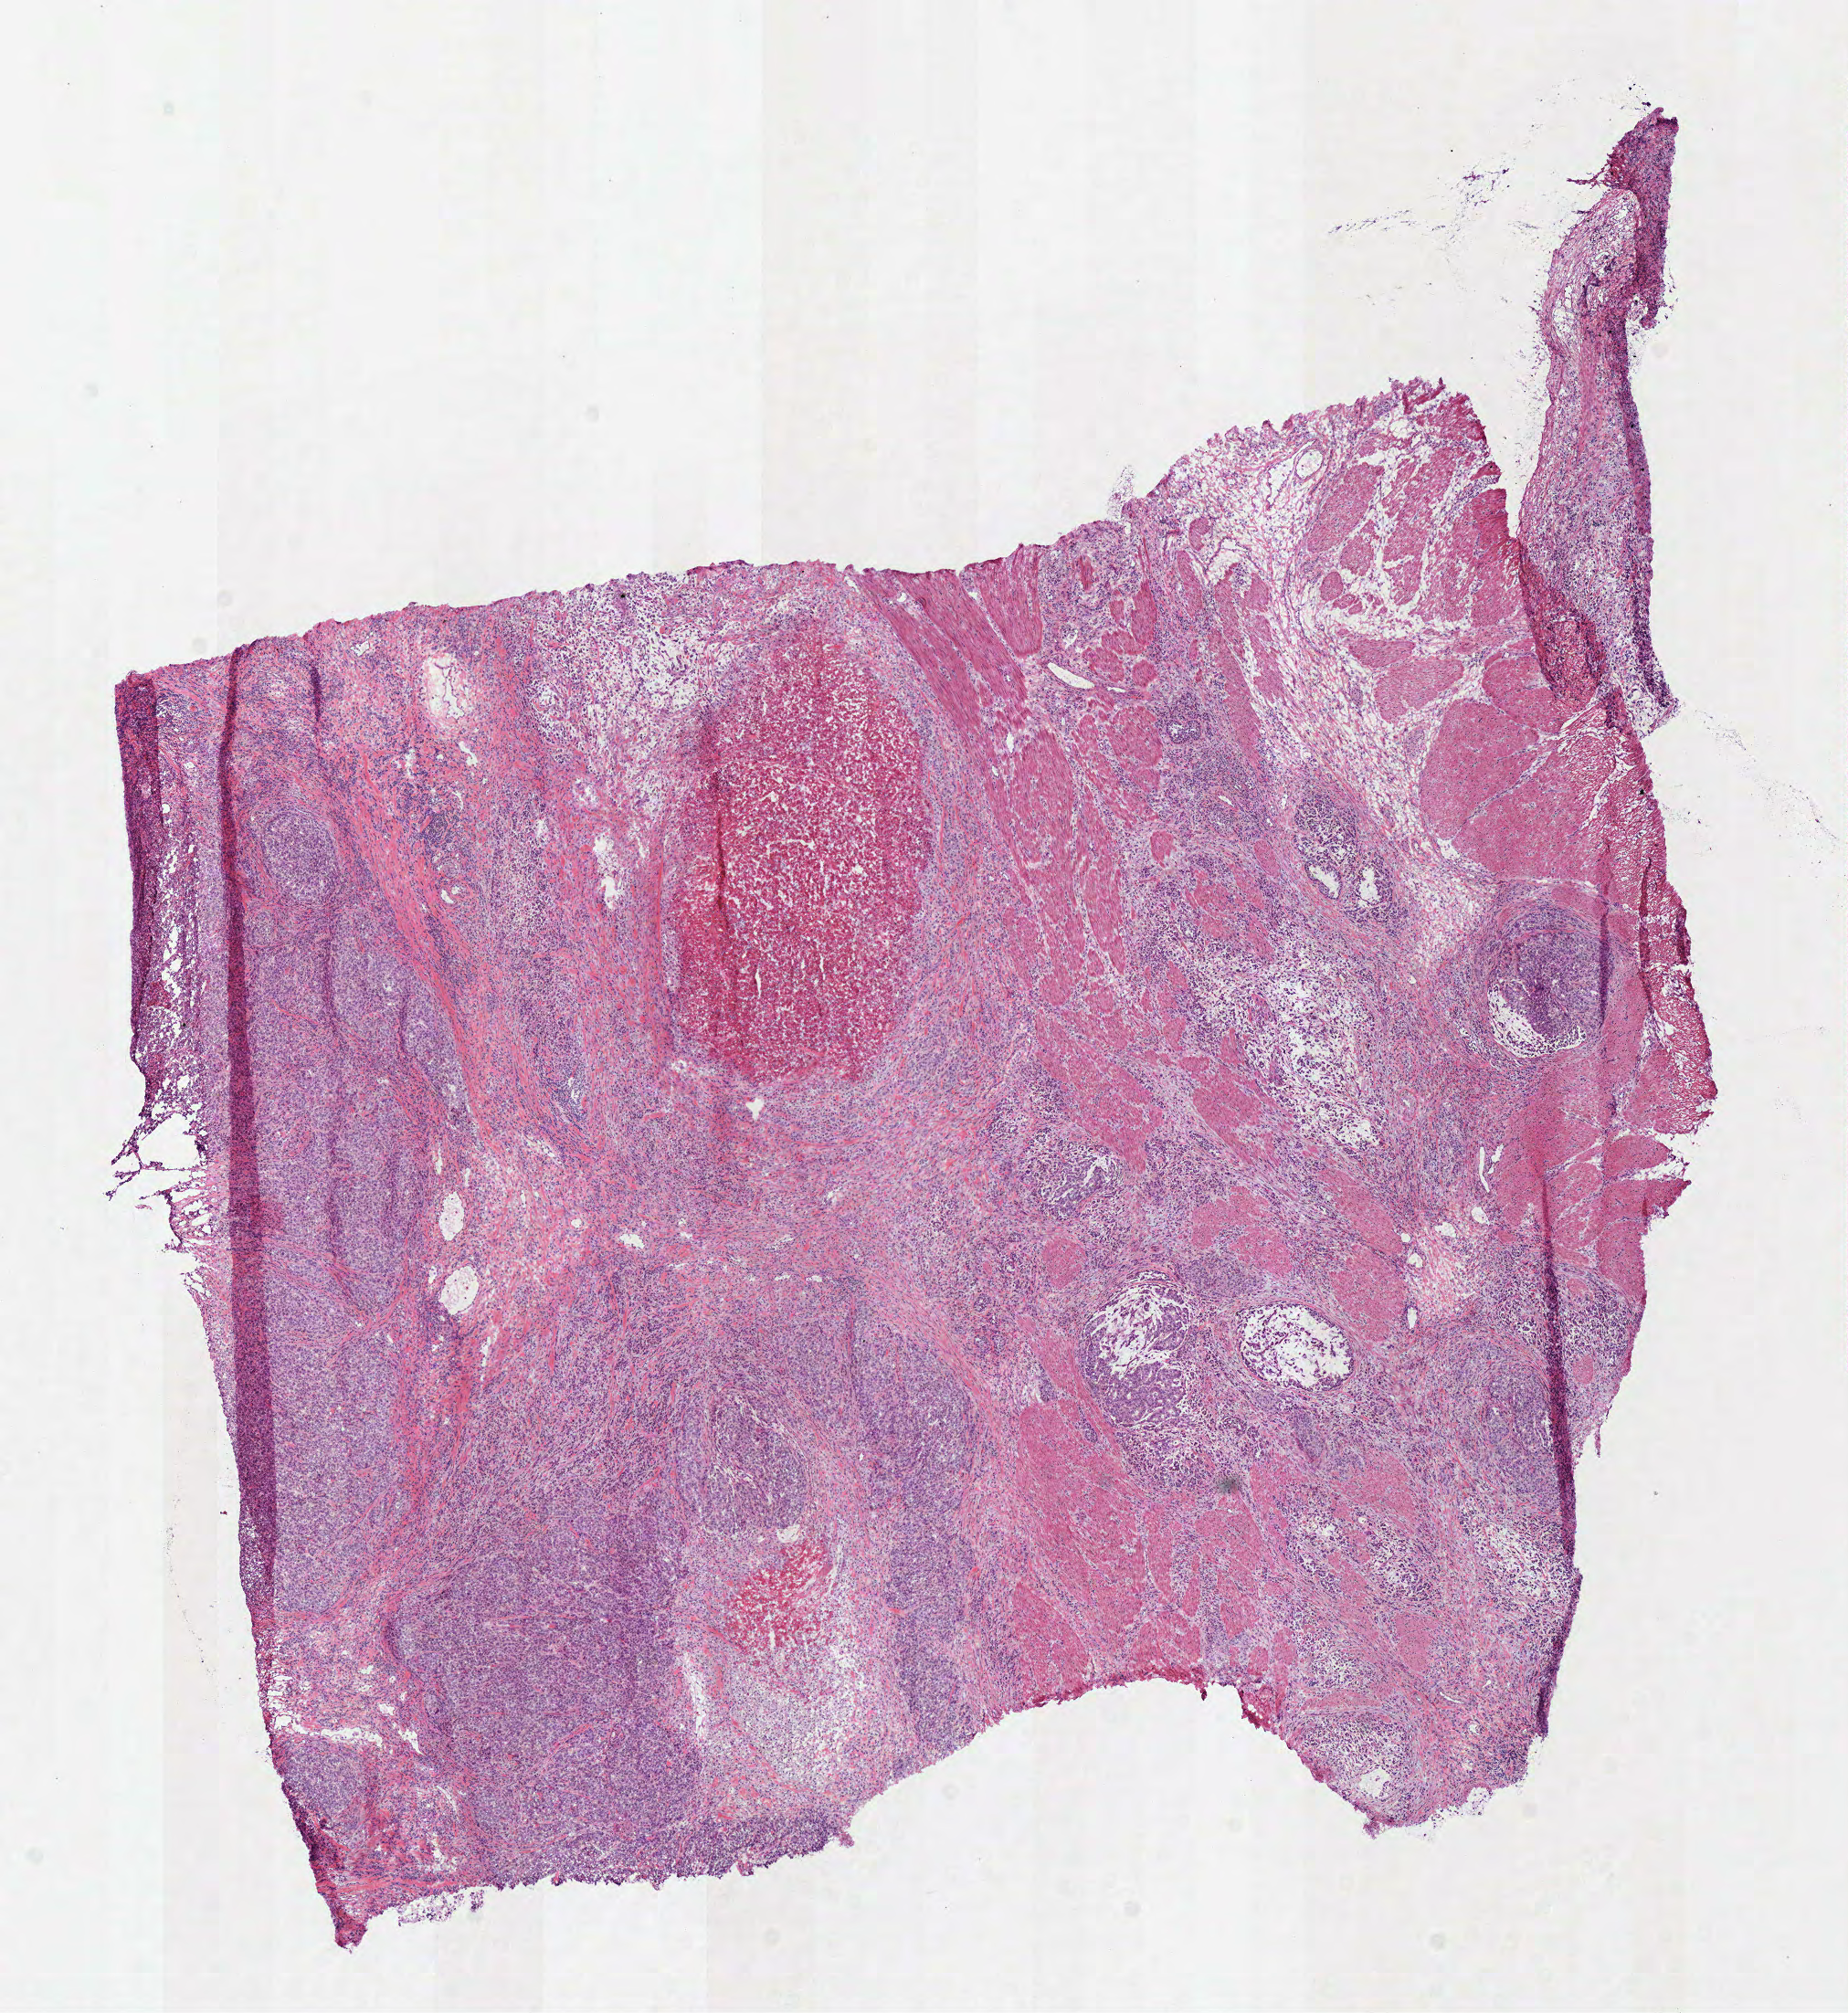
H&E whole-slide image, shown as a low-resolution overview of the whole scanned area (about 8.0 x 8.7 mm, slide scanned at 40x); frozen section; sample: primary tumour, stomach. Male patient; age at initial diagnosis 53 years. Histologic grade: G3 (poorly differentiated). Slide review estimates, as recorded: tumour cells 82%, tumour nuclei 65%, normal cells 0%, stromal cells 10%, necrosis 8%.
• lymph nodes positive (case pathology): 11 of 22 examined
• pathologic diagnosis: Carcinoma, diffuse type (body of stomach)
• AJCC pathologic stage: IIIA (7th edition)